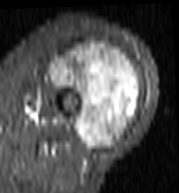
MRI of an extremity soft-tissue mass, one axial slice; position 52 of 103 along the scan axis; STIR; MR volume resampled by the dataset authors to the PET/CT grid (not the native acquisition matrix); 3.27 mm slice thickness; 179 × 193 image matrix. Female patient. Case-level facts recorded for this patient, not image findings: histological type: undifferentiated – high grade; grade: high; site of the primary tumour: left thigh.
Structures marked on this image (expert contour drawn on MRI and transferred to this co-registered scan by the dataset authors):
- gross tumour volume including surrounding oedema: bounding box (x1, y1, x2, y2) in pixels: (48, 42, 142, 150)
- gross tumour volume (mass): (50, 42, 140, 150)